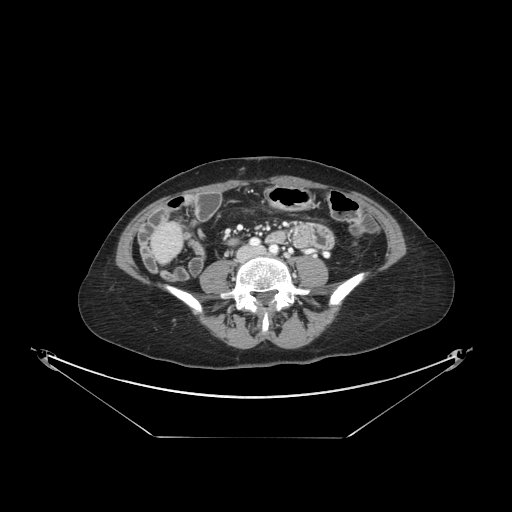
Contrast-enhanced abdominal CT, one axial slice. Slice 20 of 148 in the series (ordered by position). 120 kVp. Intravenous contrast given. Soft-tissue window (W 400 / L 40 HU). 2.5 mm slice thickness. 512 × 512 image matrix. Female patient, age 73 years. From the clinical record (not read from this slice): diagnosis: colorectal cancer liver metastases, imaged before liver resection; multiple liver metastases: no; largest metastasis: 1 cm; disease in both lobes: no.
Structures marked on this image (outlined manually by an expert reader):
- liver: bounding box <154,226,181,260> (left, top, right, bottom; pixels)